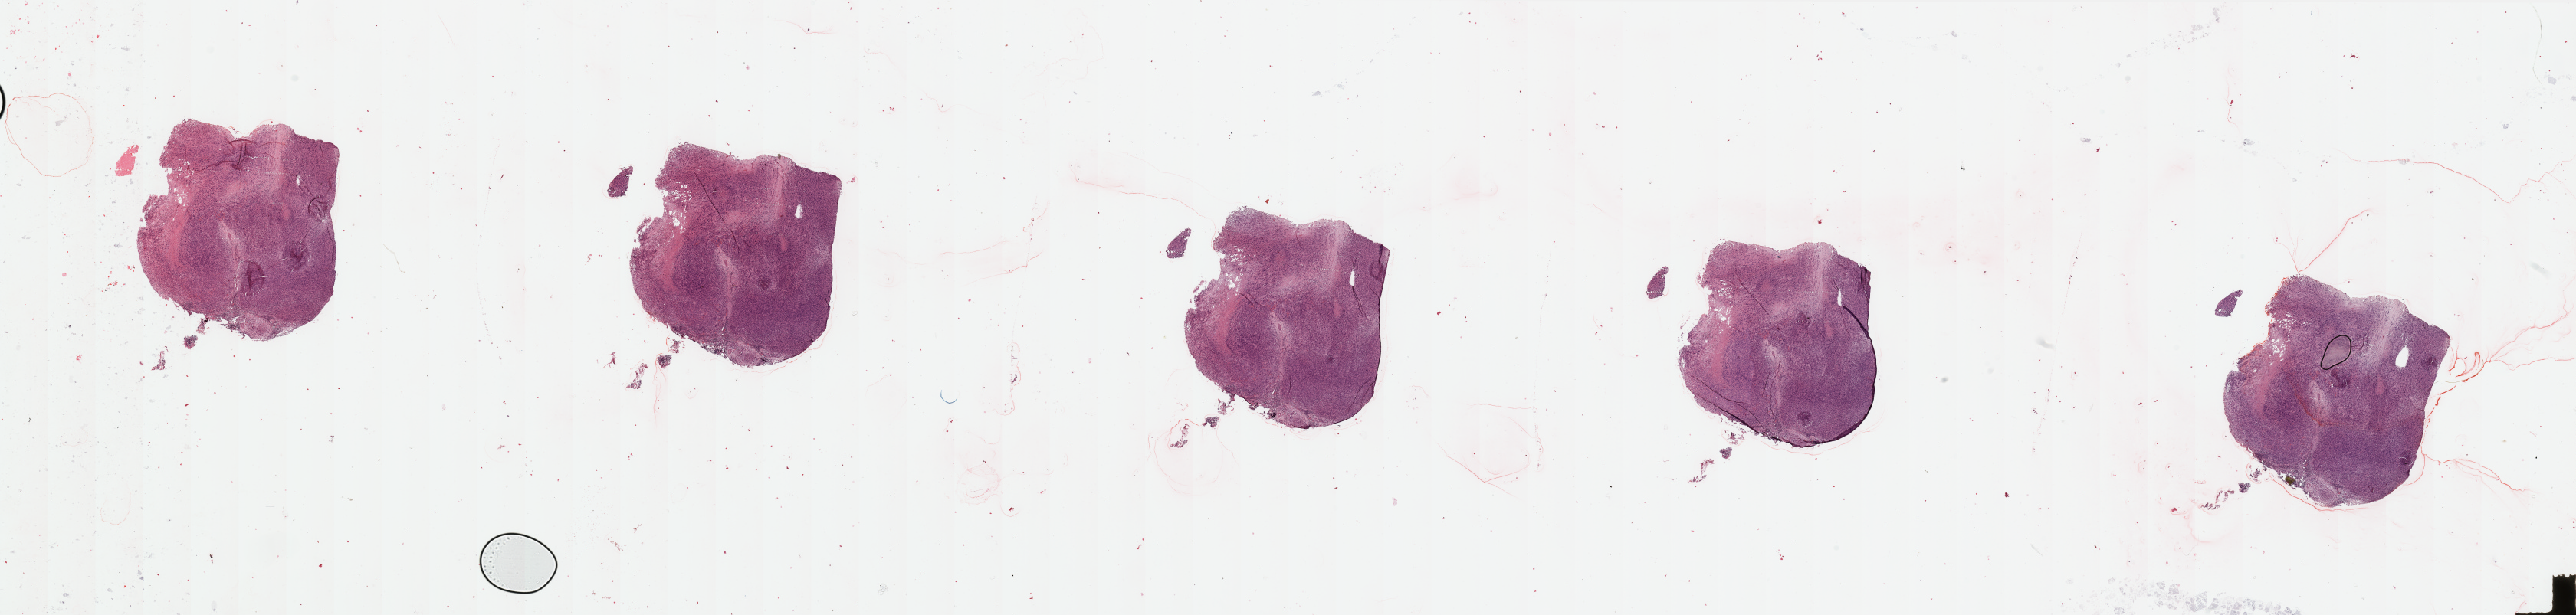
Whole-slide histology image, H&E — low-resolution overview of the scanned area, about 53.2 x 12.7 mm. Tumour tissue sample, sampled site: lymph node. 84-year-old male patient.
Patient diagnosis: Malignant melanoma, NOS.